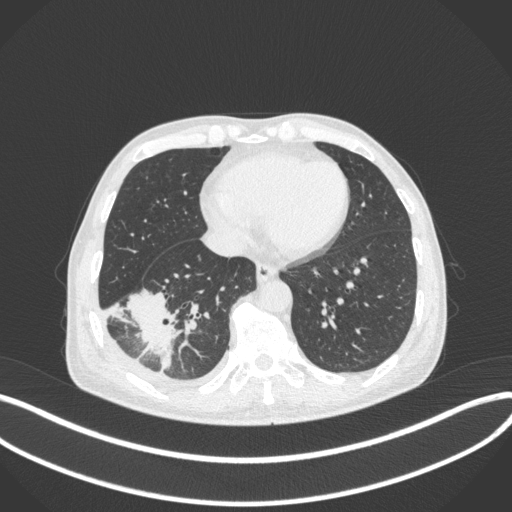
Chest CT, one axial slice; slice 121 of 385 in the series (ordered by position); lung window (W 1500 / L -600 HU); 1 mm slice thickness; 512 × 512 image matrix, field of view 400 × 400 mm. Patient: male, 64 years. Case-level facts recorded for this patient, not image findings: clinical TNM (as recorded): T3 N0 M0; histopathological grade: G2-3.
Structures marked on this image (rectangle marked by the reading radiologist):
- lung tumour (recorded histology: adenocarcinoma): bounding box <126,282,176,376> (left, top, right, bottom; pixels)